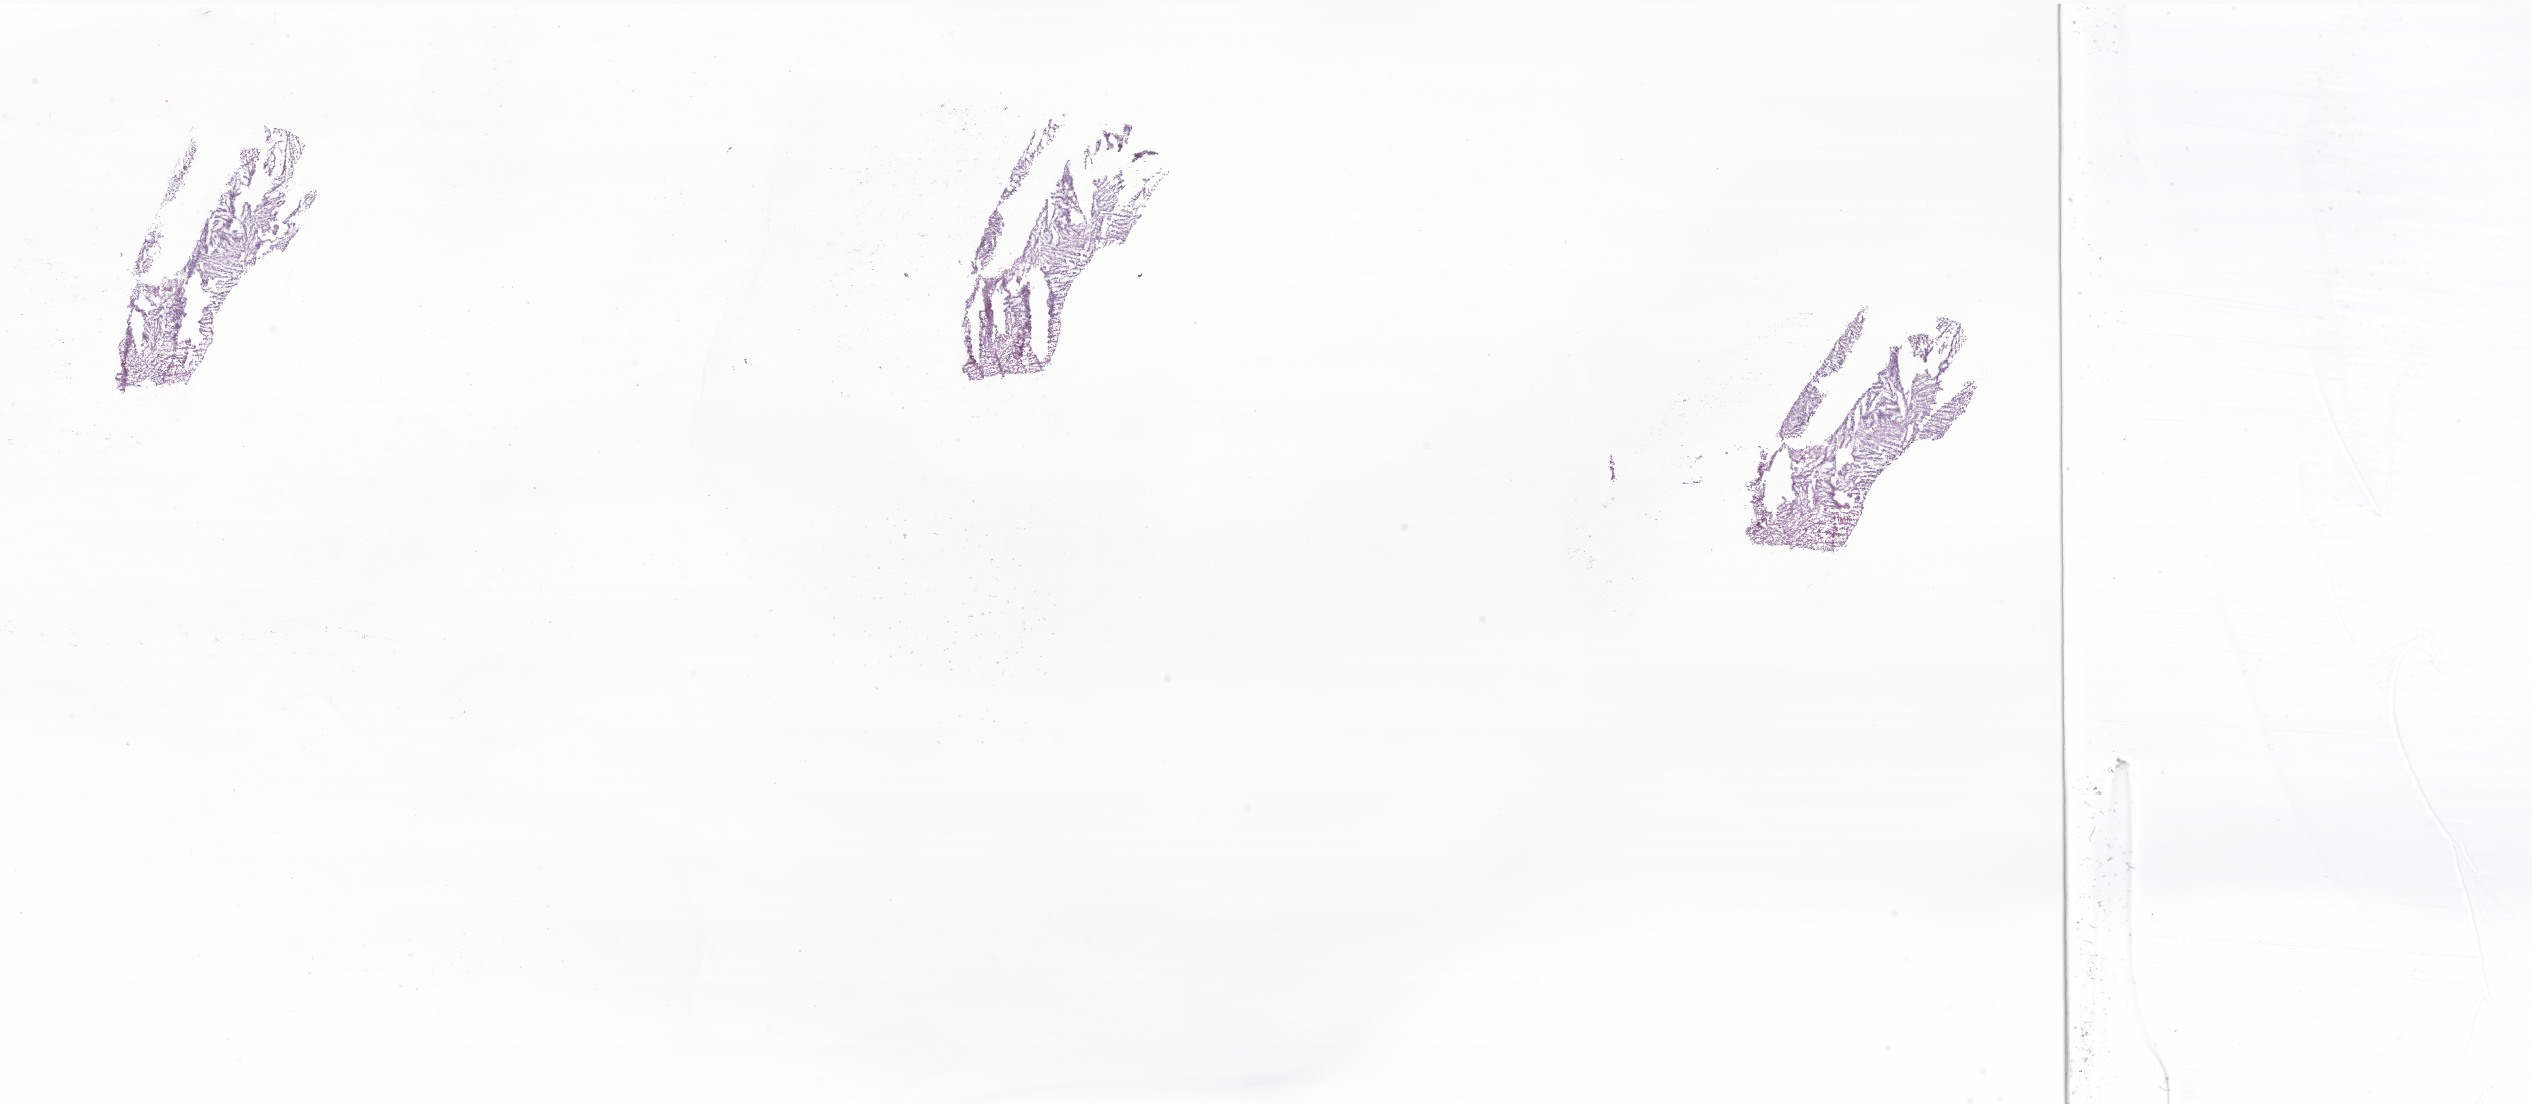
Haematoxylin and eosin whole-slide image of tumor tissue from the brain, a low-resolution overview of the entire scanned area, about 42.7 x 18.6 mm. Cryosection (OCT / tissue freezing medium). Male patient, age 107 months (8 years 11 months).
Diagnosis: Neuroblastoma, NOS.